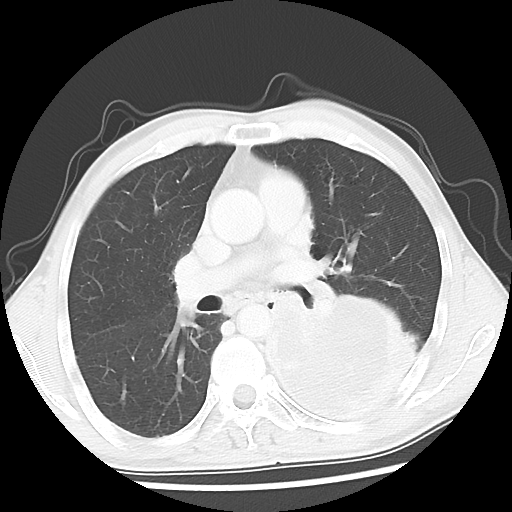
Chest CT, one axial slice; slice 28 of 52 in the series (ordered by position); lung window (W 1500 / L -600 HU); 5 mm slice thickness; 512 × 512 image matrix, field of view 318 × 318 mm. Male patient, age 60 years. From the clinical record (not read from this slice): clinical TNM (as recorded): T4 N0 M0.
Outlined on this slice (bounding box drawn by a radiologist):
- lung tumour (recorded histology: squamous cell carcinoma): bounding box [x1, y1, x2, y2] px = [256, 292, 421, 418]